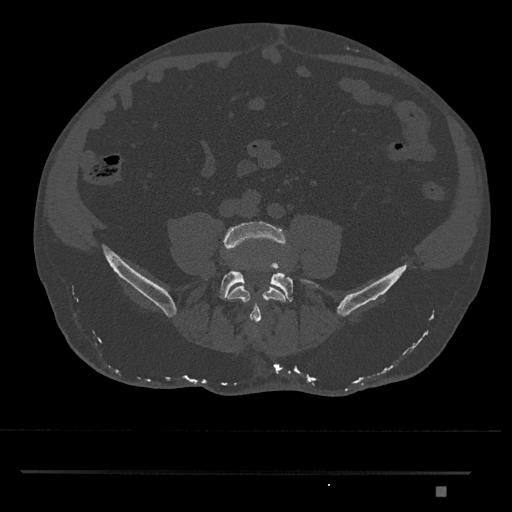
CT including the spine, one axial slice. Slice 582 of 1134 in the series (ordered by position). Bone window (W 1800 / L 400 HU). 0.5 mm slice thickness. 512 × 512 image matrix. Patient: male, 65 years. From the clinical record (not read from this slice): primary cancer: prostate.
Structures marked on this image (semi-automatically segmented with operator editing):
- L4 vertebra: box from (x=222, y=221) to (x=290, y=325) px
- L5 vertebra: (x=219, y=265)–(x=320, y=302)